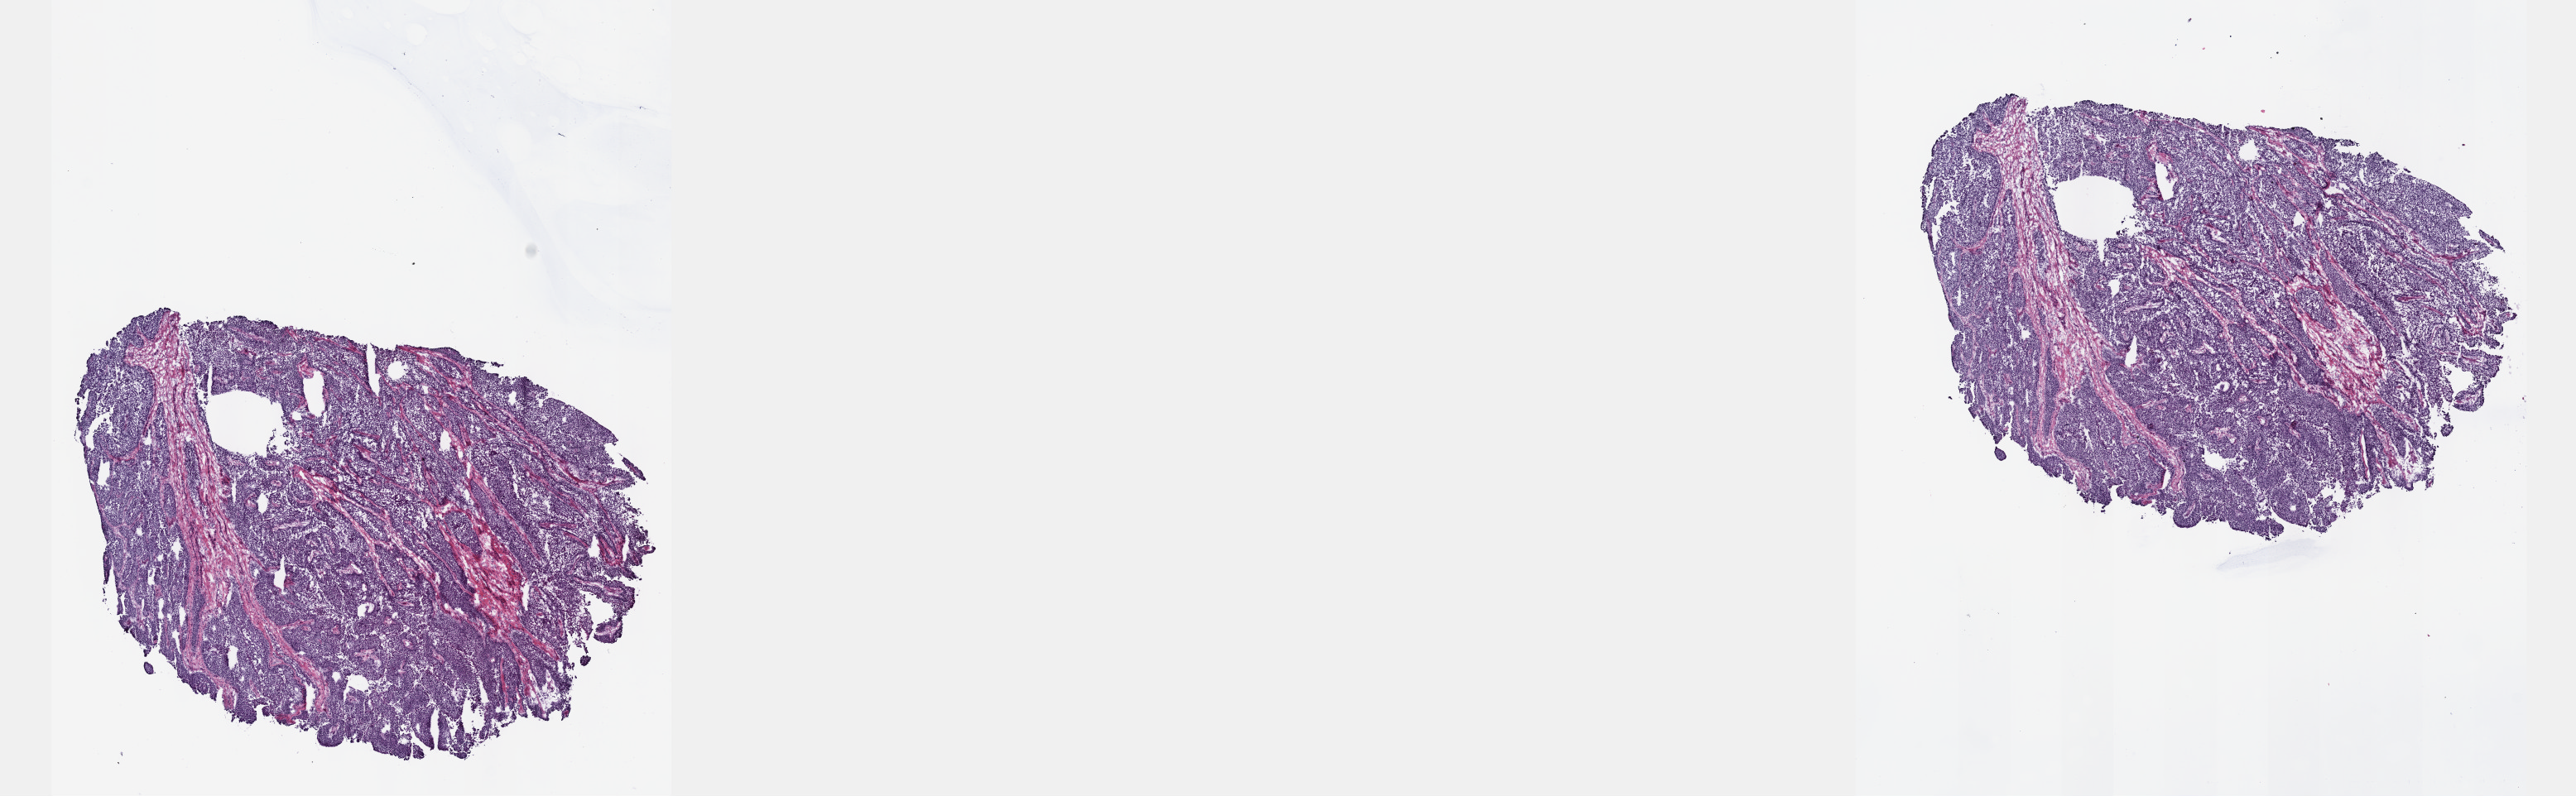
H&E-stained whole-slide image, a low-resolution overview of the entire scanned area, about 25.1 x 7.8 mm. Frozen section from the top of the tissue portion. Primary tumour sample from the bladder. Female patient; age at initial diagnosis 47 years.
Diagnosis: Transitional cell carcinoma (lateral wall of bladder).